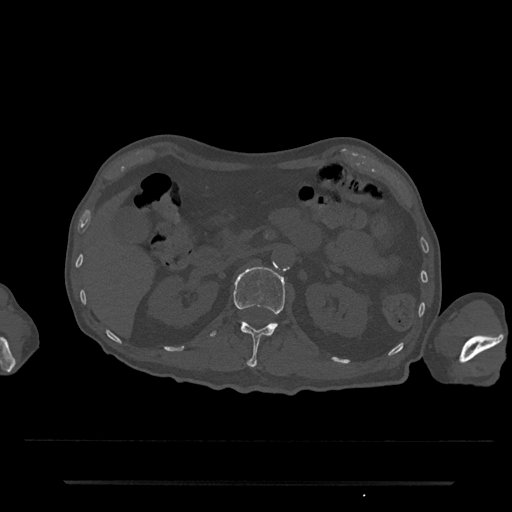
CT including the spine, one axial slice. Slice 123 of 797 in the series (ordered by position). Reconstruction kernel Br40s/3. 120 kVp. Bone window (W 1800 / L 400 HU). 512 × 512 image matrix. Male patient, age 74 years. Case-level facts recorded for this patient, not image findings: primary cancer: prostate.
Annotated regions visible in this slice (semi-automatically segmented with operator editing):
- L1 vertebra: bounding box (x1, y1, x2, y2) in pixels: (207, 267, 285, 367)